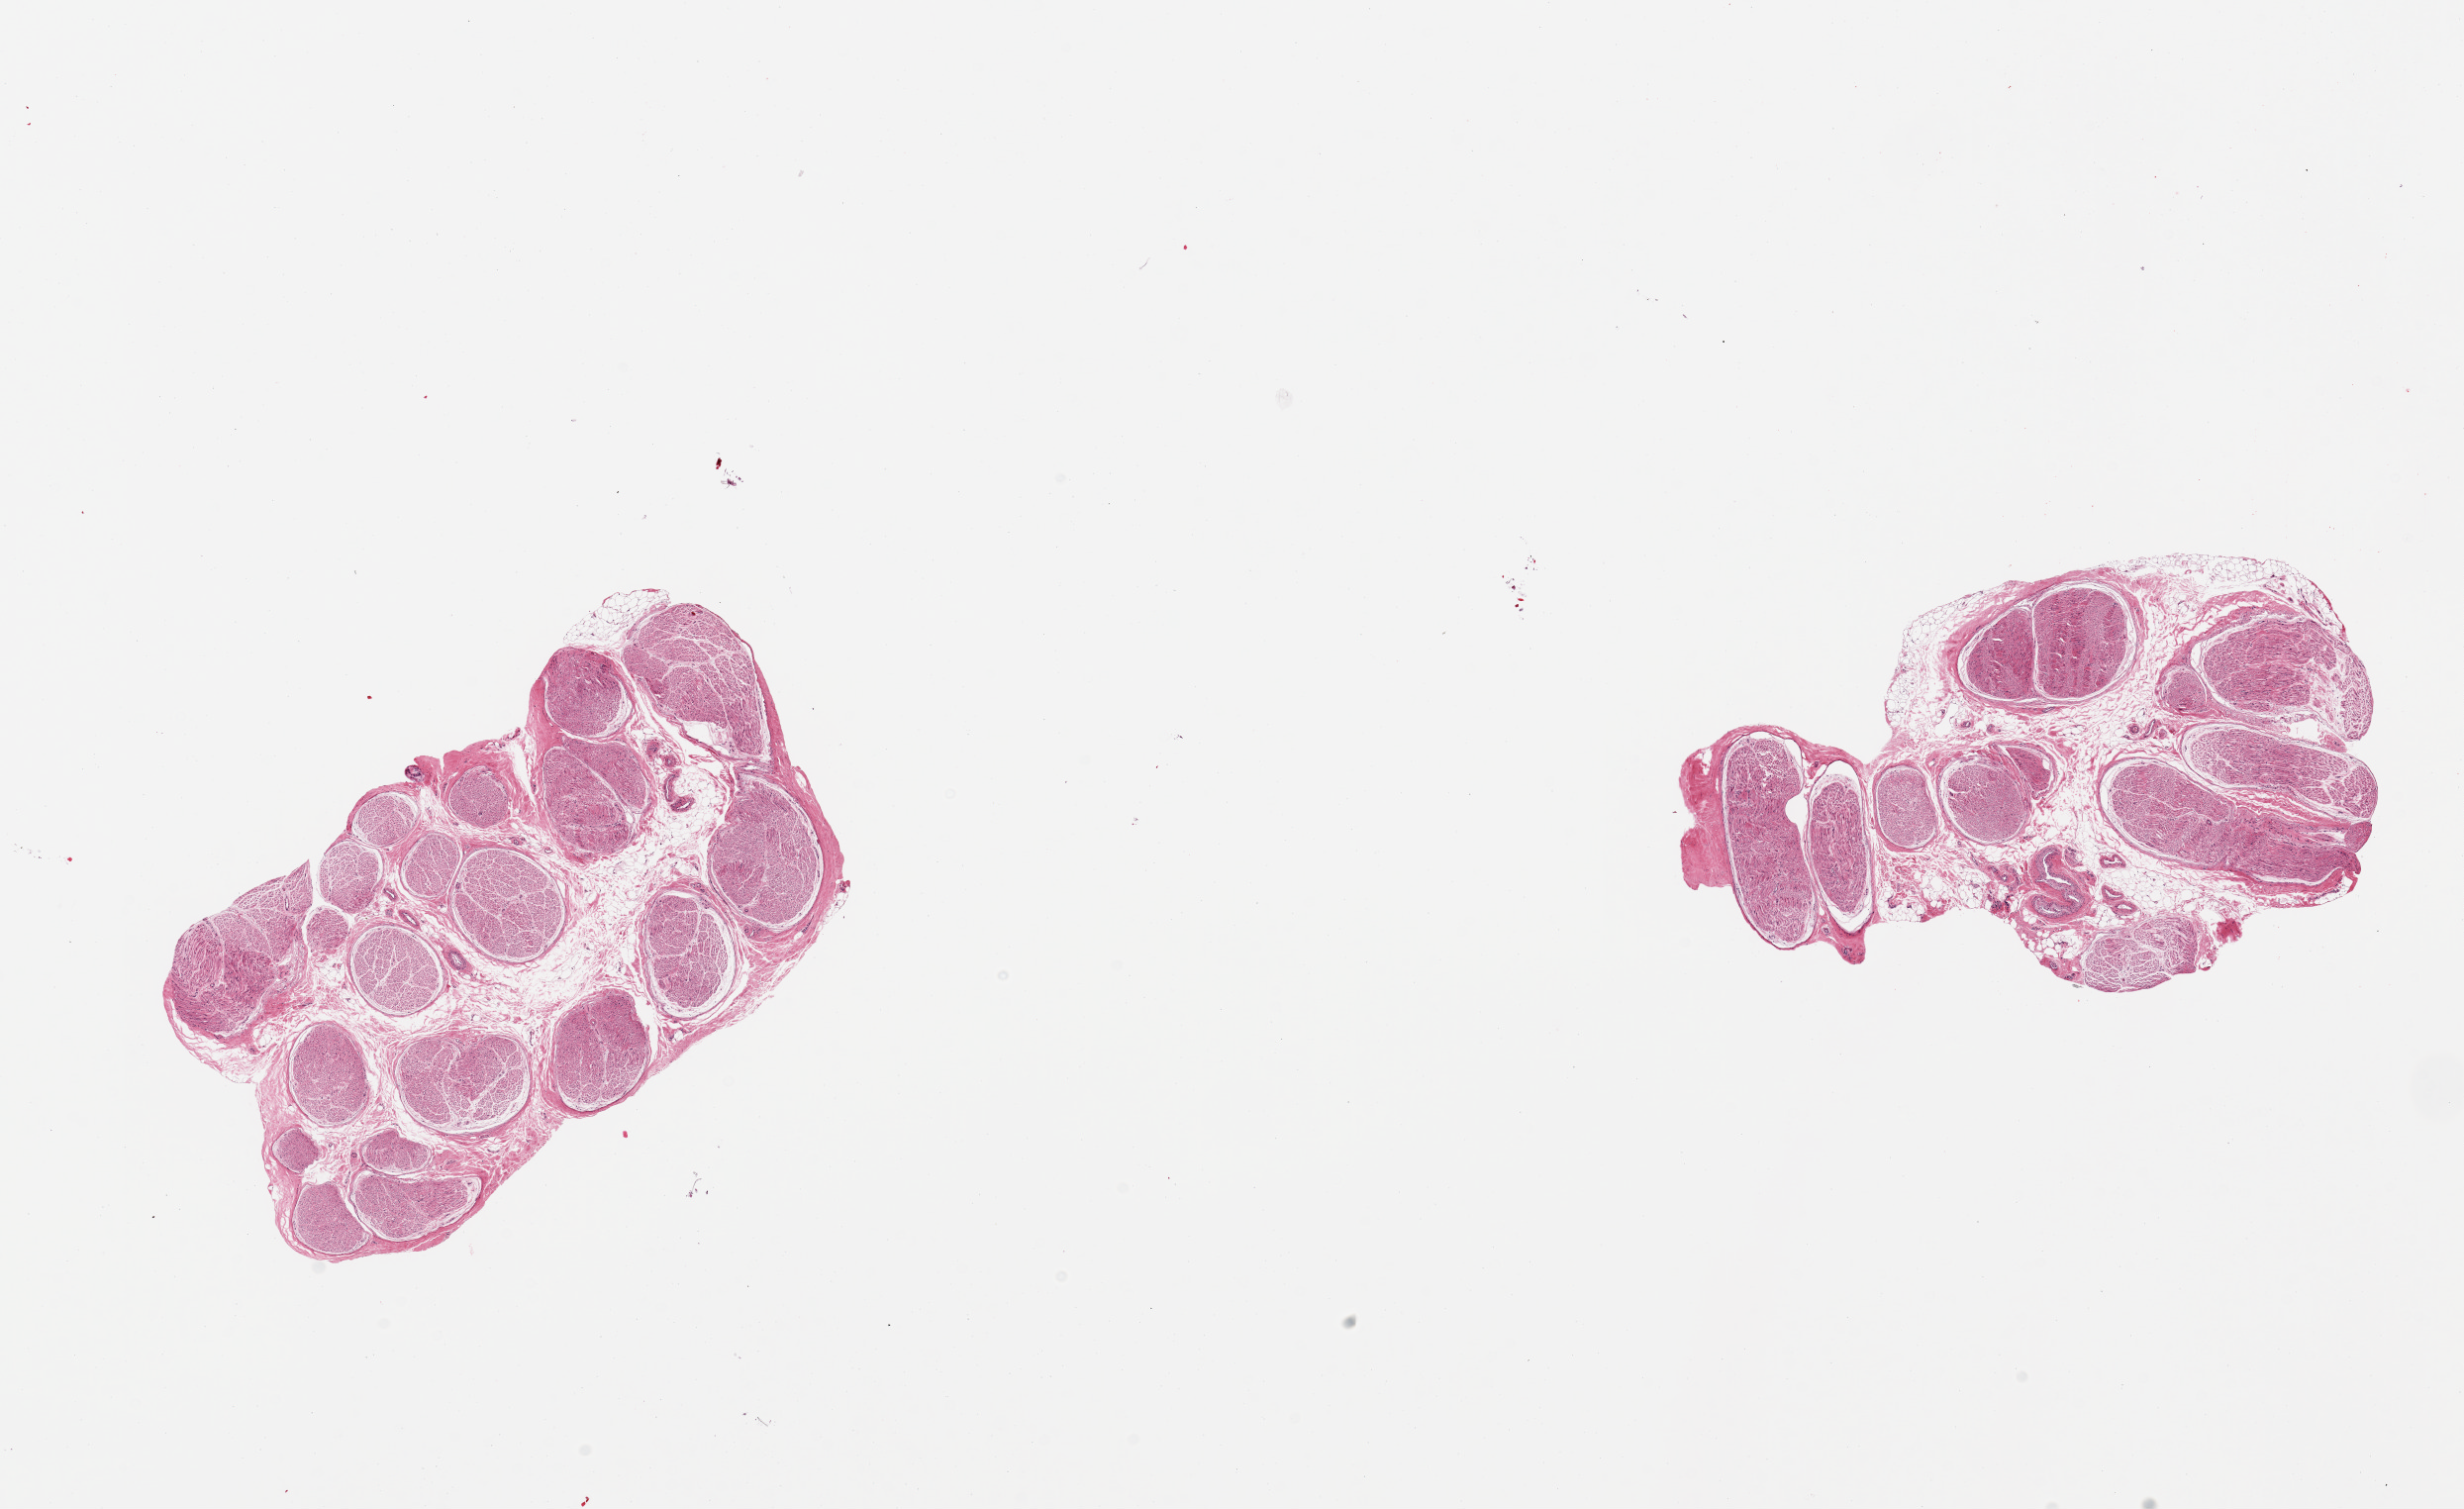
Digitized haematoxylin and eosin-stained section, shown as a low-resolution overview of the whole scanned area (about 19.7 x 12.1 mm, acquisition: 20x scan), PAXgene-fixed paraffin-embedded (PFPE) section, sampled site (target tissue): tibial nerve, tissue donor sample. Donor sex: female.
Pathologist's review note for this sample: 2 pieces, nog significant adherent fat, clean specimens.